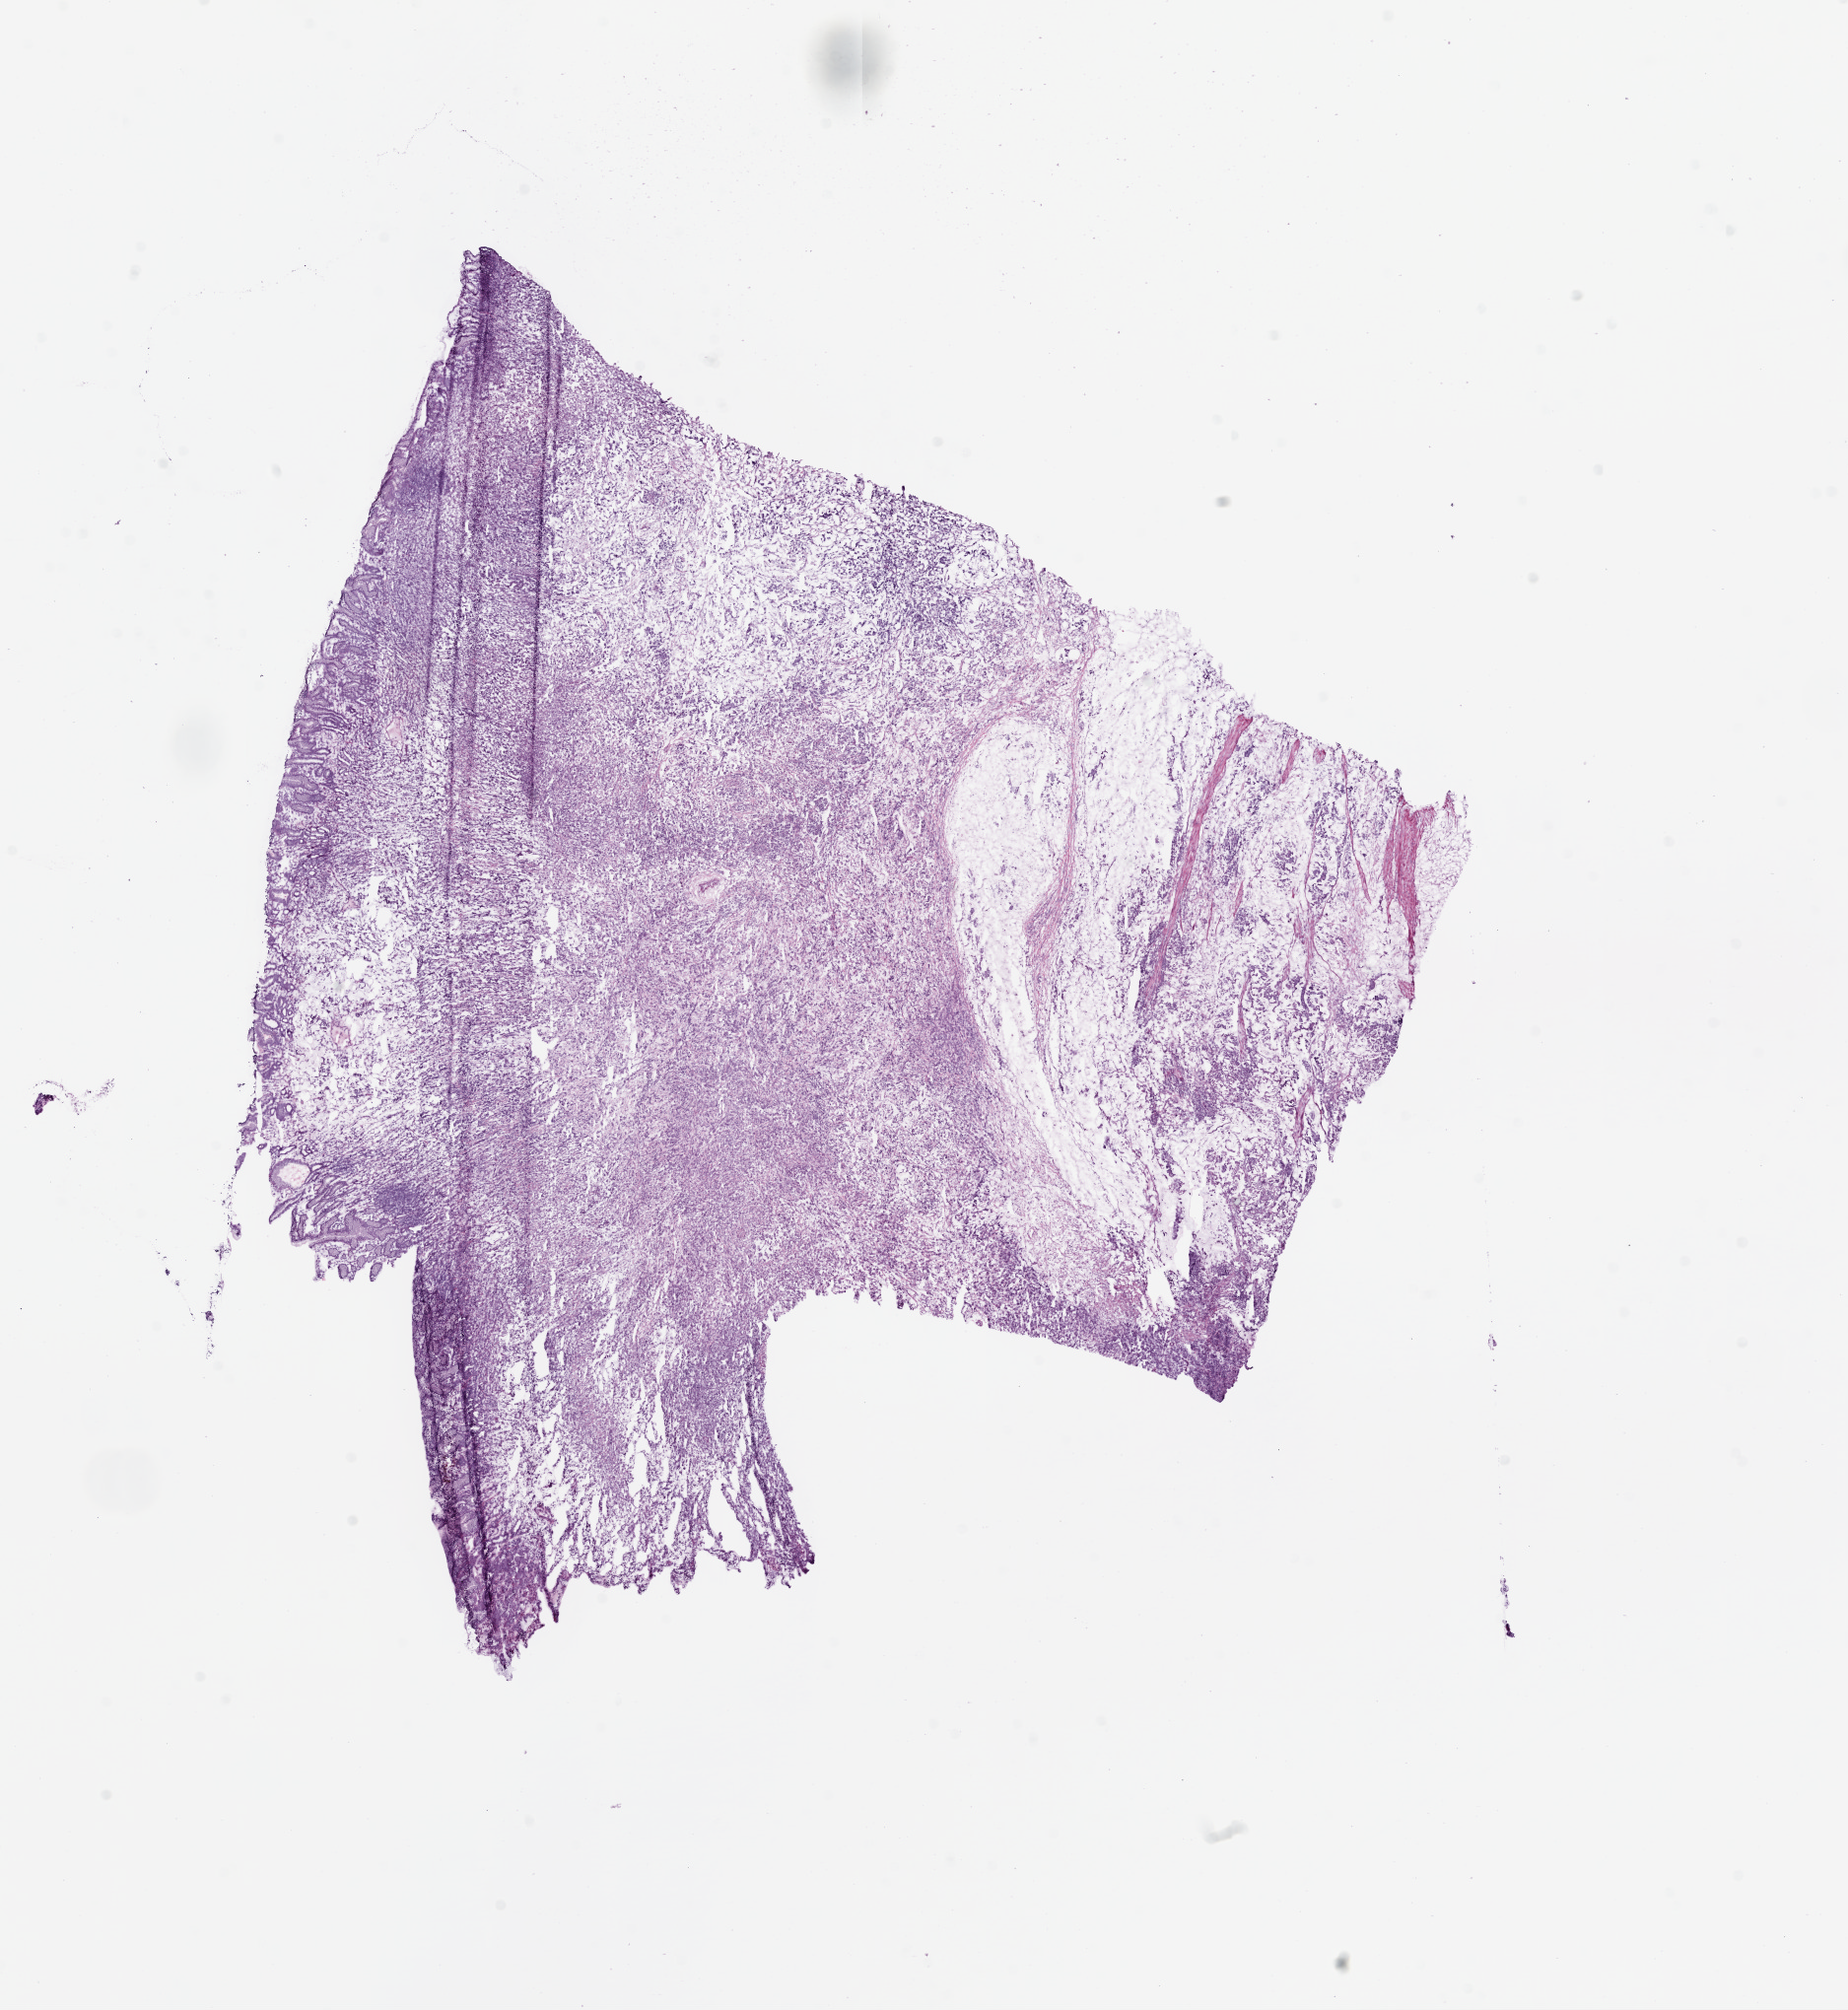
Digitized H&E tissue section (whole slide), a low-resolution overview of the entire scanned area, about 15.0 x 16.4 mm; frozen section; stomach, primary tumour sample. Female patient; age at initial diagnosis 67 years. Histologic grade: G3 (poorly differentiated). Slide review estimates, as recorded: tumour cells 80%, tumour nuclei 70%, normal cells 10%, stromal cells 10%, necrosis 0%.
Lymph nodes positive (case pathology): 6 of 39 examined. Diagnosis: Carcinoma, diffuse type. TNM: T4a N2 M1. AJCC pathologic stage: IV (7th edition).